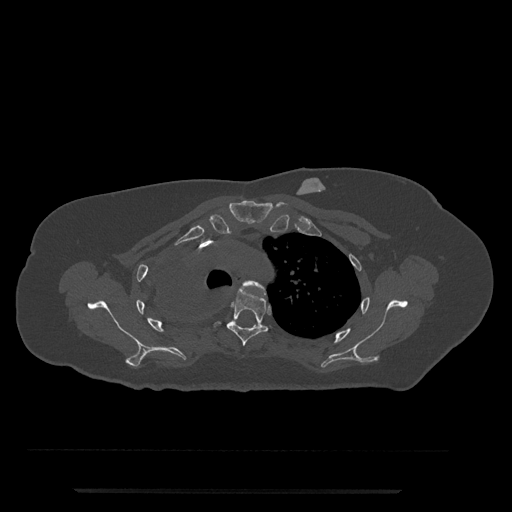
CT including the spine, one axial slice; slice 592 of 797 in the series (ordered by position); reconstruction kernel Br40s/3; 120 kVp; bone window (W 1800 / L 400 HU); 0.5 mm slice thickness; 512 × 512 image matrix, field of view 440 × 440 mm. Patient: female, 51 years. From the clinical record (not read from this slice): primary cancer: neuro.
Outlined on this slice (semi-automatic segmentation, software-assisted and operator-edited):
- T3 vertebra: bounding box <242,280,265,292> (left, top, right, bottom; pixels)
- T4 vertebra: <215,286,273,346>